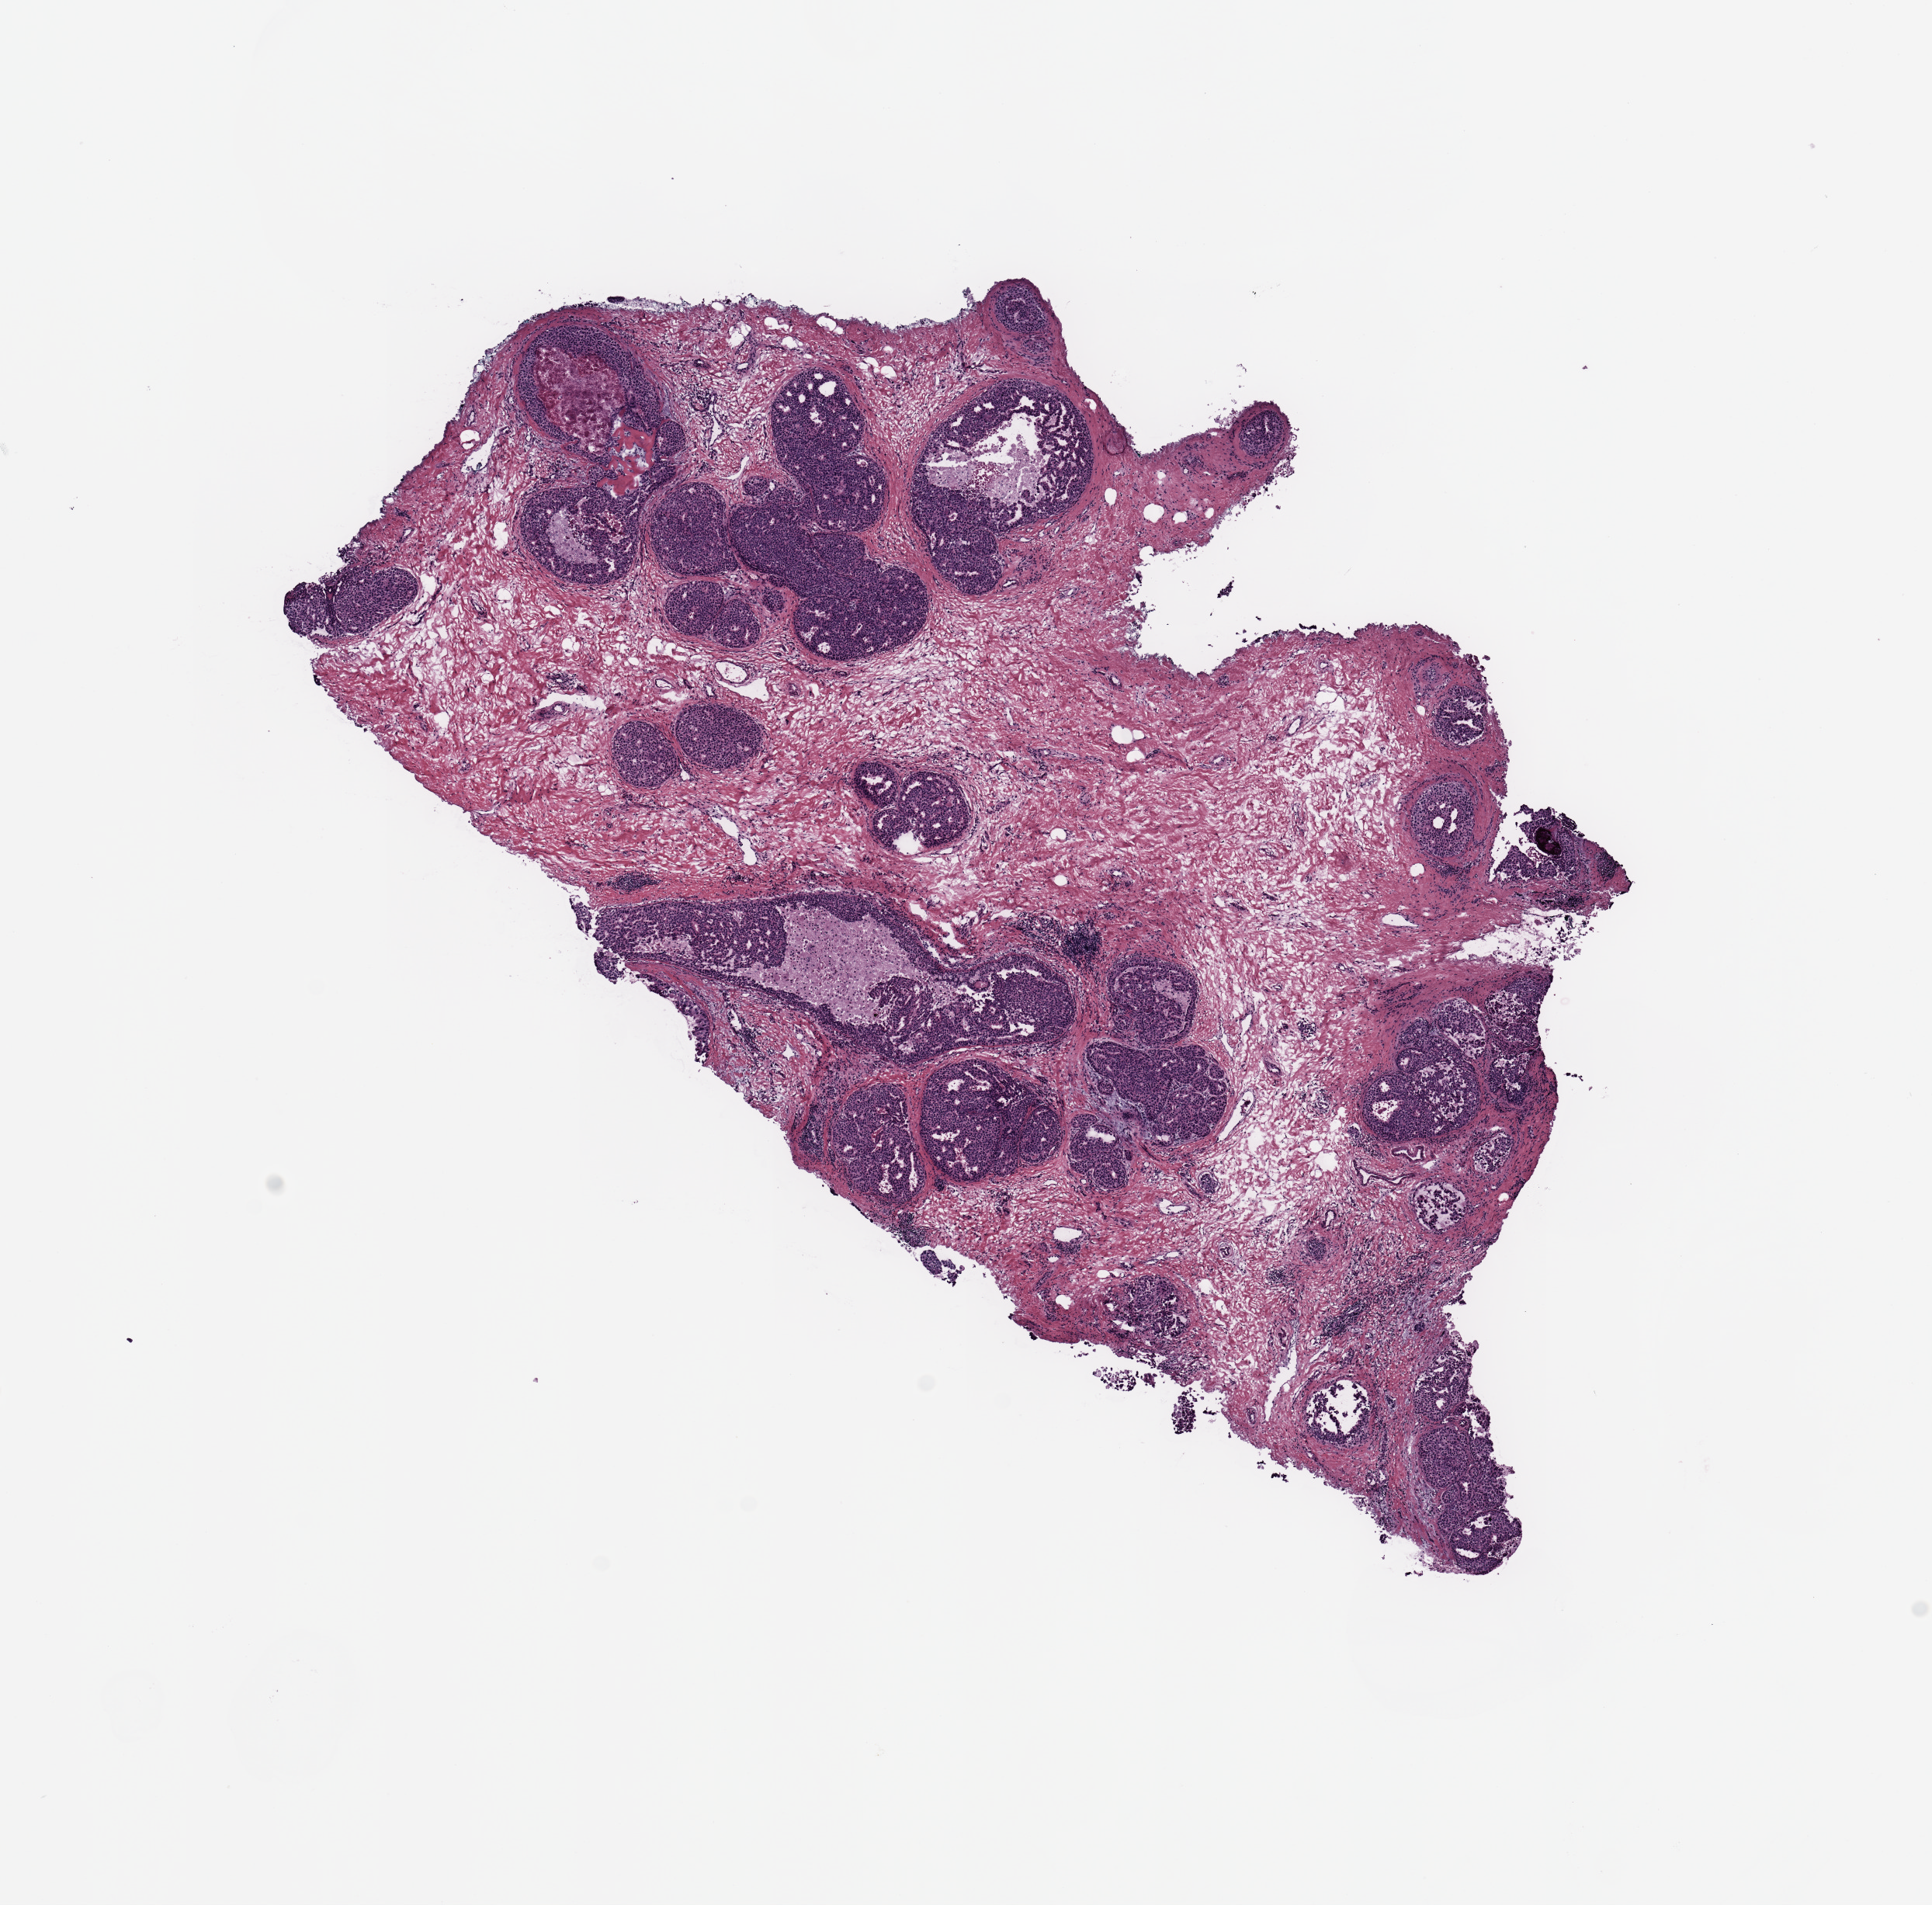
Digitized Hematoxylin and eosin (H&E) stained tissue section (whole slide) — whole scanned area (about 9.8 x 9.7 mm, from a 20x scan) shown as a low-resolution overview, breast, tissue type not recorded.
Patient diagnosis (cohort enrolment): breast cancer (breast).